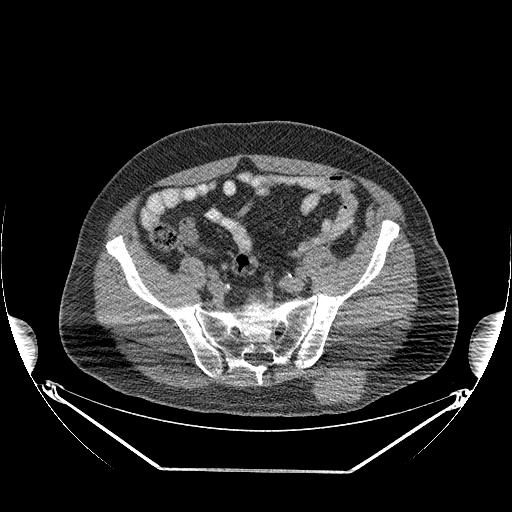
CT of an extremity soft-tissue mass (from a PET/CT study), one axial slice; slice 85 of 267 in the series (ordered by position); 140 kVp; soft-tissue window (W 400 / L 40 HU); 3.75 mm slice thickness; 512 × 512 image matrix. Male patient. Case-level facts recorded for this patient, not image findings: histological type: pleiomorphic leiomyosarcoma; grade: high; site of the primary tumour: left buttock.
Annotated regions visible in this slice (expert contour drawn on MRI and transferred to this co-registered scan by the dataset authors):
- gross tumour volume including surrounding oedema: box from (x=311, y=368) to (x=368, y=405) px
- gross tumour volume (mass): (x=315, y=370)–(x=366, y=405)